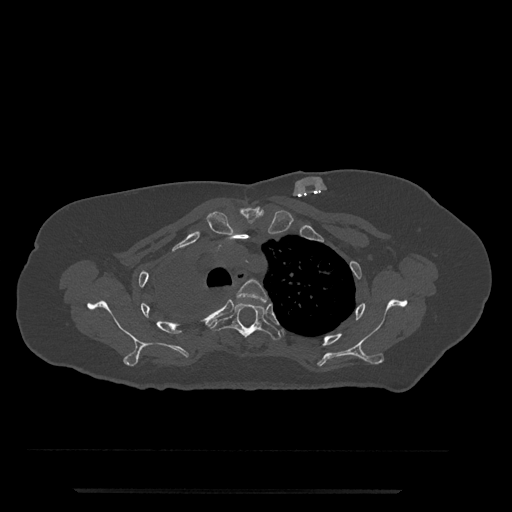
CT including the spine, one axial slice. Slice 602 of 797 in the series (ordered by position). Reconstruction kernel Br40s/3. 120 kVp. Bone window (W 1800 / L 400 HU). 0.5 mm slice thickness. 512 × 512 image matrix, field of view 440 × 440 mm. Female patient, age 51 years. Case-level facts recorded for this patient, not image findings: primary cancer: neuro; vertebrae with lytic lesions (as recorded): T8.
Outlined on this slice (semi-automatically segmented with operator editing):
- T3 vertebra: bounding box (x1, y1, x2, y2) in pixels: (236, 279, 268, 303)
- T4 vertebra: (210, 303, 282, 340)